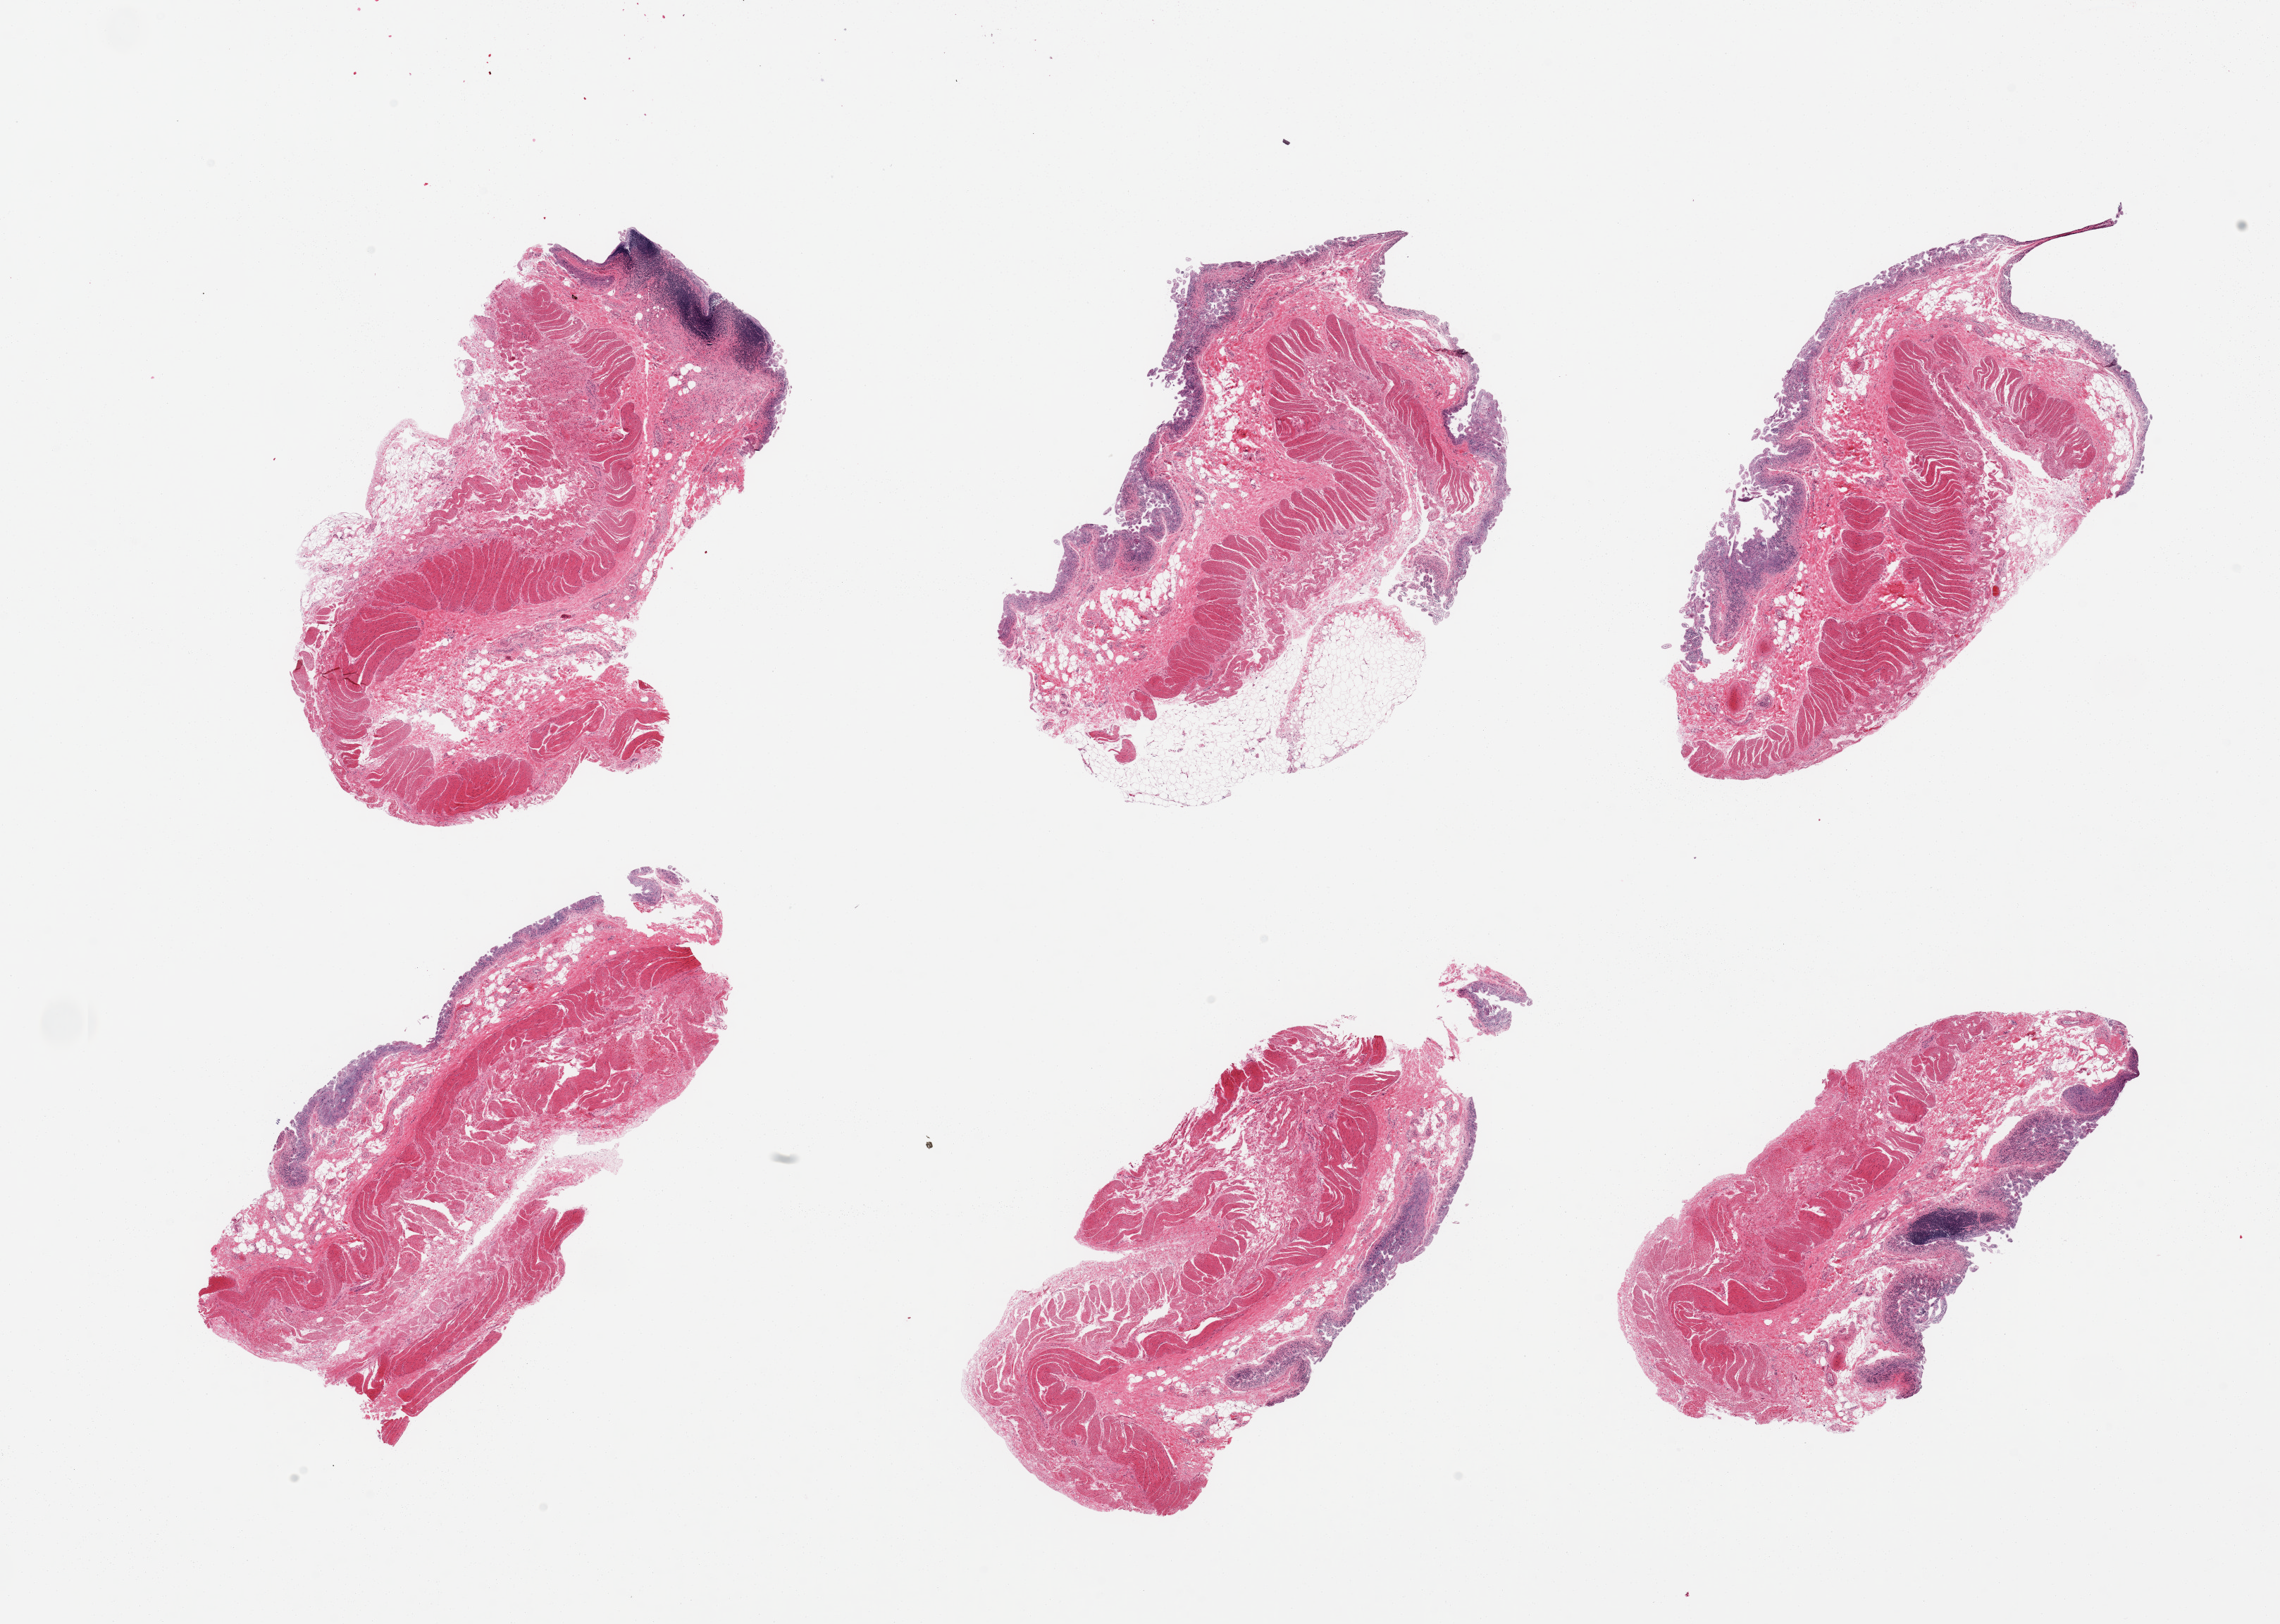
H&E whole-slide image, low-resolution overview of the scanned area, about 25.6 x 18.2 mm; PAXgene-fixed paraffin-embedded (PFPE) section; sampled site (target tissue): ileum; donor tissue sample. Donor sex: male.
Review note (as recorded): 6 pieces; full thickness sections (muscularis not target), lymphoid nodules are scattered and variably preserved.